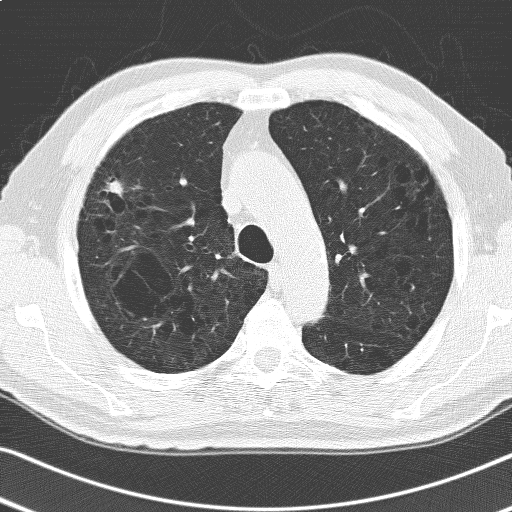
Low-dose screening chest CT, one axial slice. Position 127 of 168 along the scan axis. 120 kVp. Lung window (W 1500 / L -600 HU). 3.2 mm slice thickness. 512 × 512 image matrix.
Structures marked on this image (outlined manually by an expert reader):
- lesion 1 (tumor, upper lobe of right lung): bounding box (x1, y1, x2, y2) in pixels: (107, 181, 123, 196)